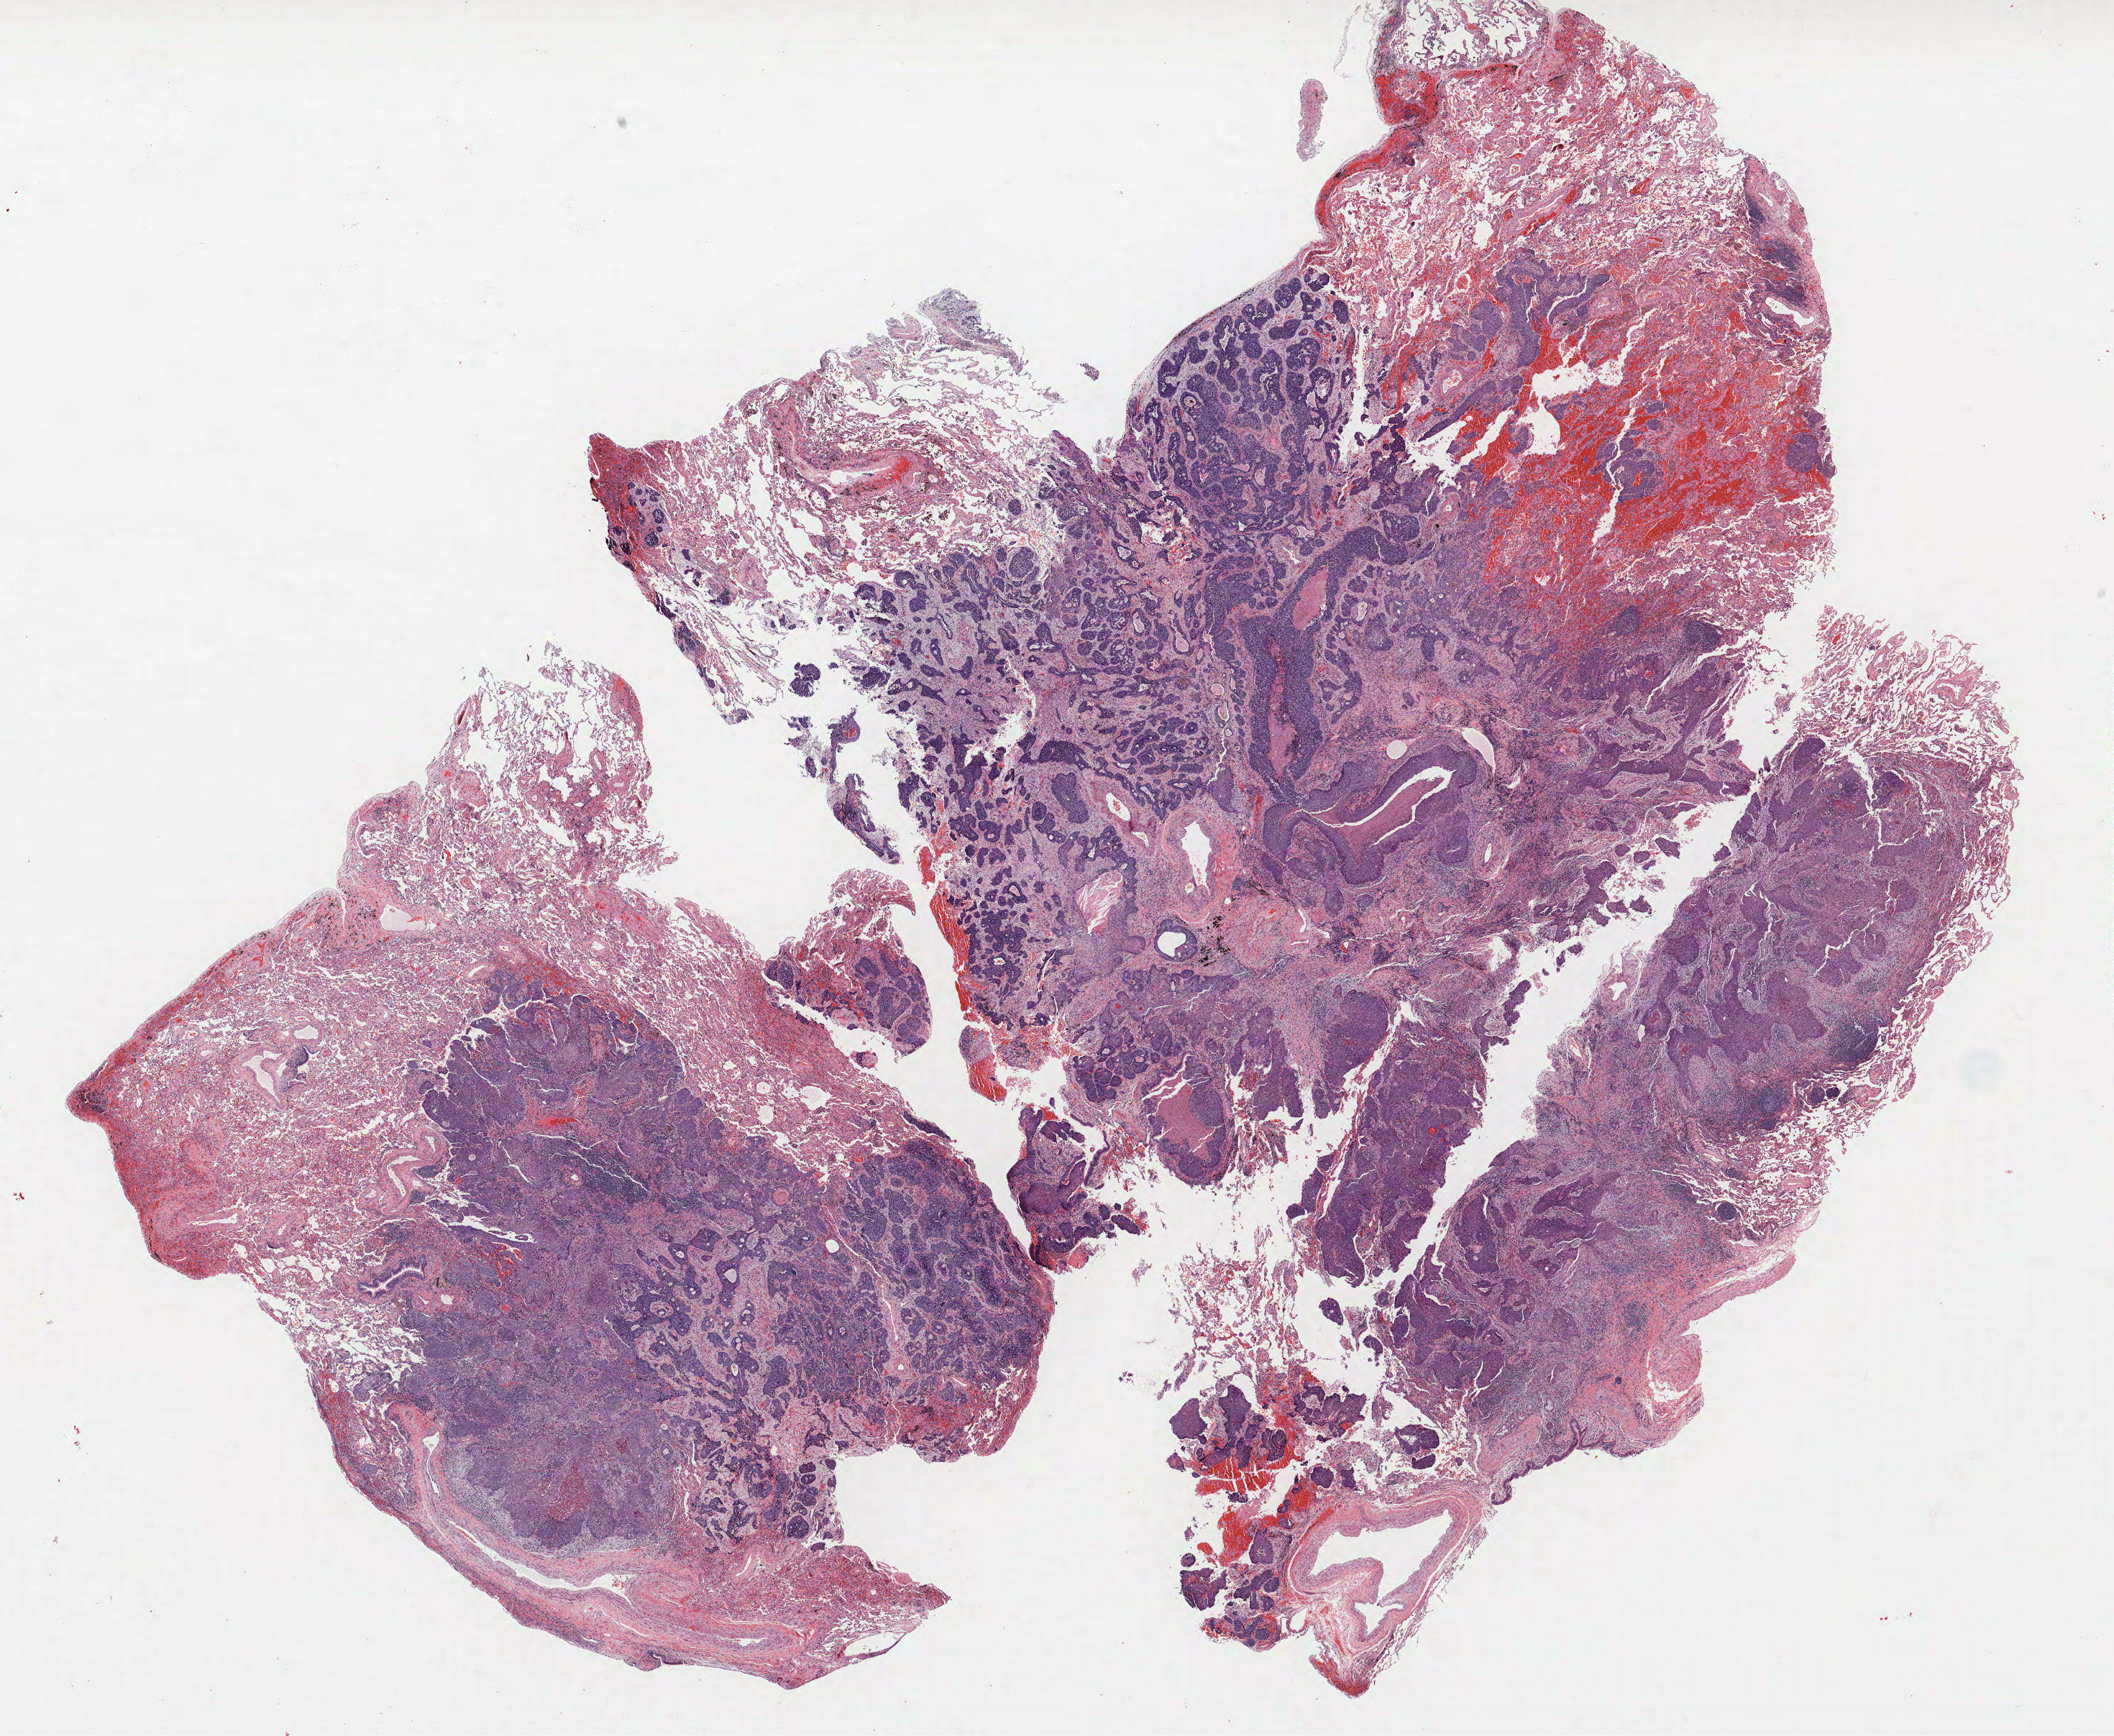
Hematoxylin and eosin (H&E) stained whole-slide image — whole scanned area (about 23.5 x 19.3 mm, acquisition: 40x scan) shown as a low-resolution overview. Formalin-fixed paraffin-embedded (FFPE) section. Lung tissue. Female, age 66 at enrolment. Current smoker at enrolment. Grade: poorly differentiated (G3).
Primary tumour location (clinical record): right upper lobe, right middle lobe. Stage (AJCC 6th edition): IA. Participant's lung-cancer diagnosis: Squamous cell carcinoma, keratinizing, NOS. Tumour size (pathology): 14 mm.